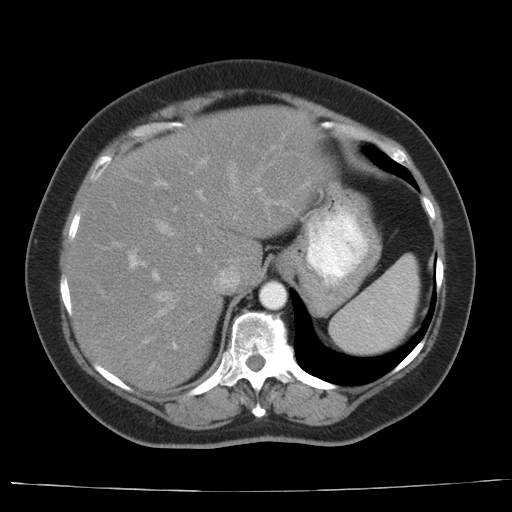
Contrast-enhanced abdominal CT, one axial slice; position 26 of 44 along the scan axis; reconstruction kernel AA-1; intravenous contrast given; soft-tissue window (W 400 / L 40 HU); 5 mm slice thickness; 512 × 512 image matrix, field of view 373 × 373 mm. Female patient. From the clinical record (not read from this slice): diagnosis: colorectal cancer liver metastases, imaged before liver resection.
Outlined on this slice (manually delineated by an expert):
- hepatic veins: bounding box [x1, y1, x2, y2] px = [155, 167, 237, 316]
- liver: [66, 107, 330, 391]
- planned liver remnant (the part of the liver to remain after resection): [98, 107, 331, 285]
- portal vein (with intrahepatic branches): [113, 181, 288, 348]